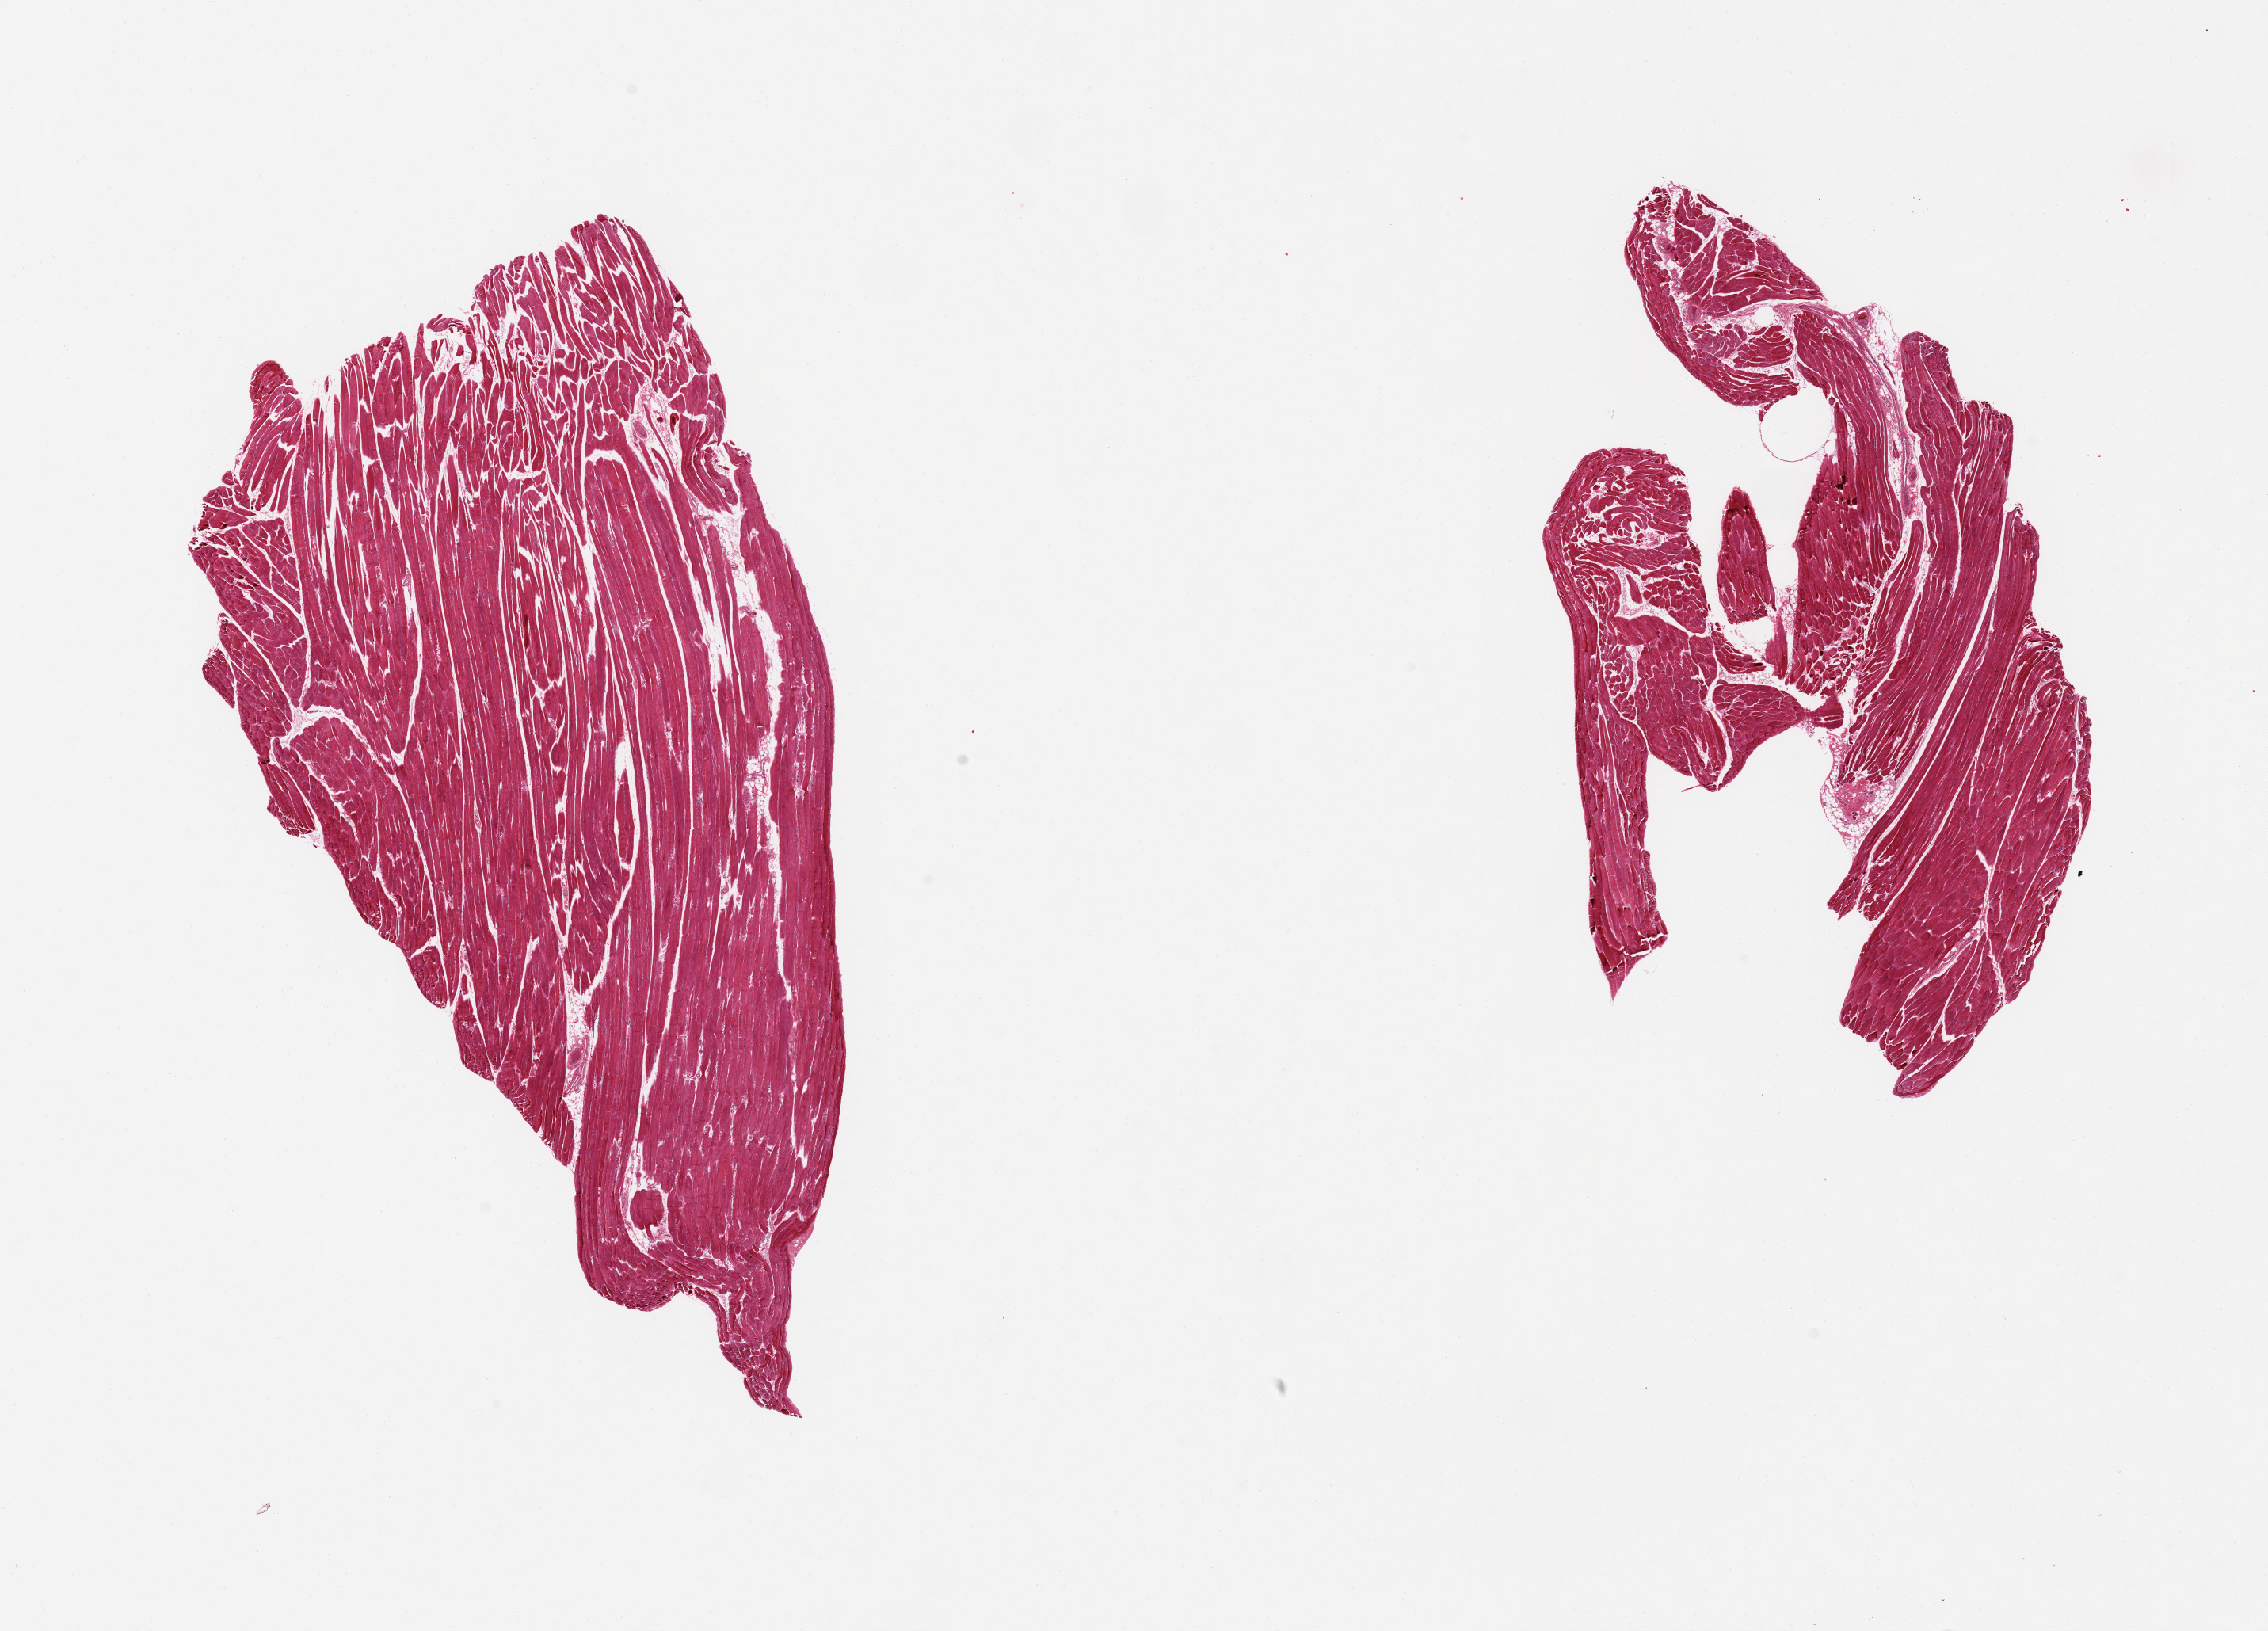
Haematoxylin and eosin whole-slide image, shown as a low-resolution overview of the whole scanned area (about 22.6 x 16.3 mm, slide scanned at 20x); PAXgene-fixed paraffin-embedded (PFPE) section; target tissue: skeletal muscle; donor tissue sample. Donor: male.
Pathologist's review note for this sample: 2 pieces.